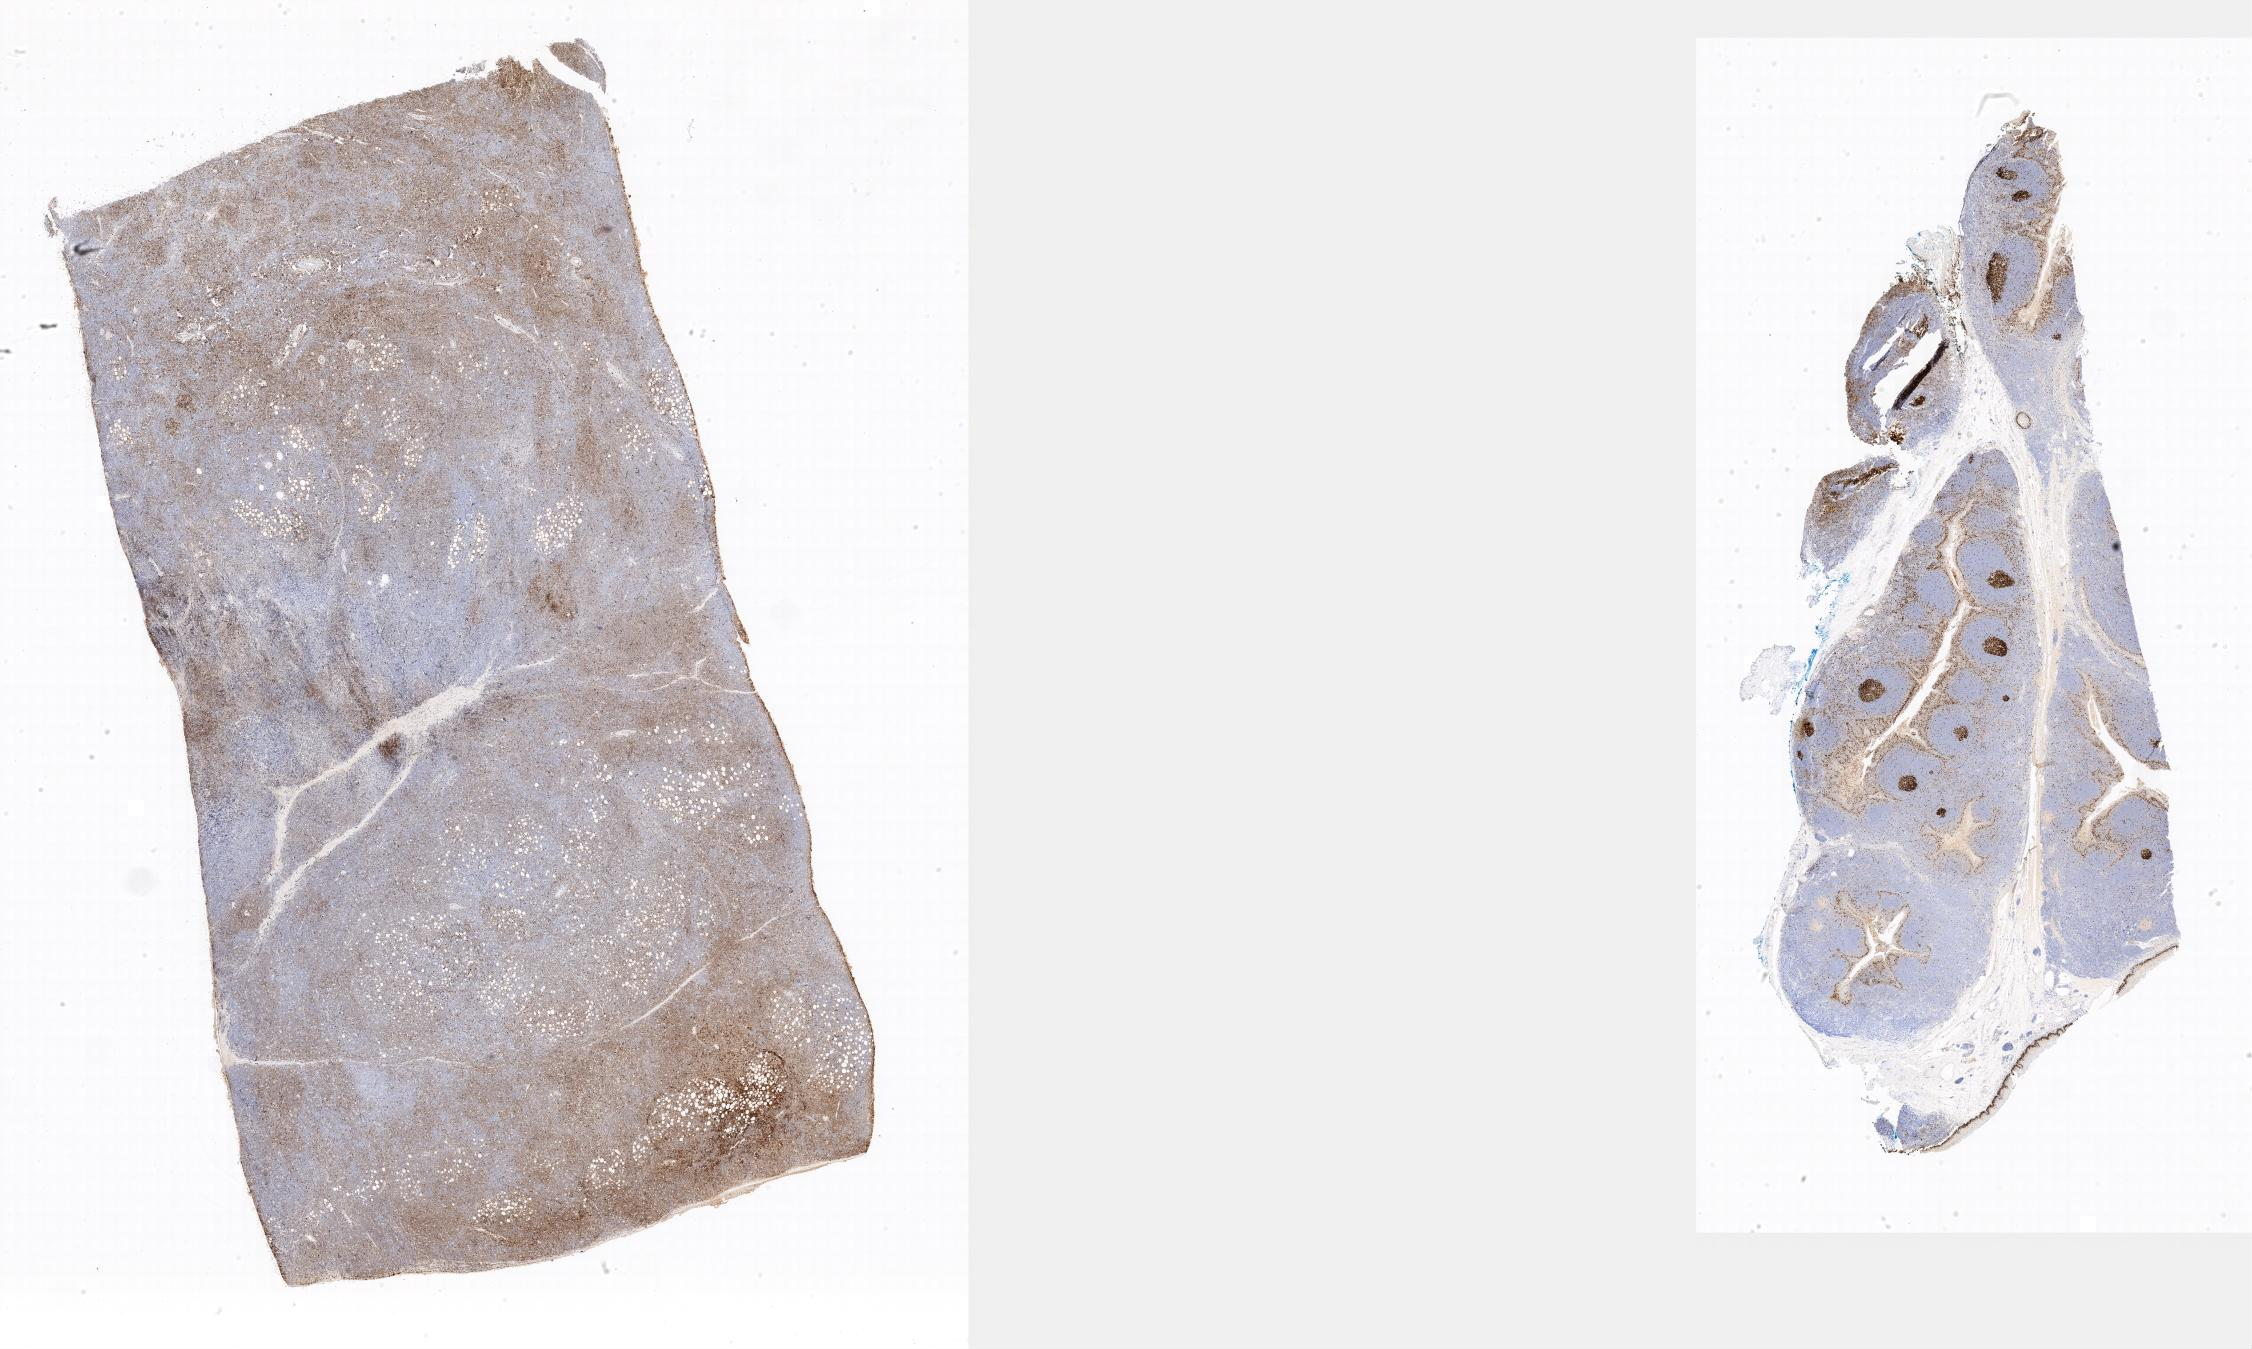
Whole-slide image, immunohistochemical stain for Ki-67, shown as a low-resolution overview of the whole scanned area; specimen: tumor tissue; anatomic site: colon. Female patient, age 12 years.
Diagnosis: Burkitt lymphoma, NOS.